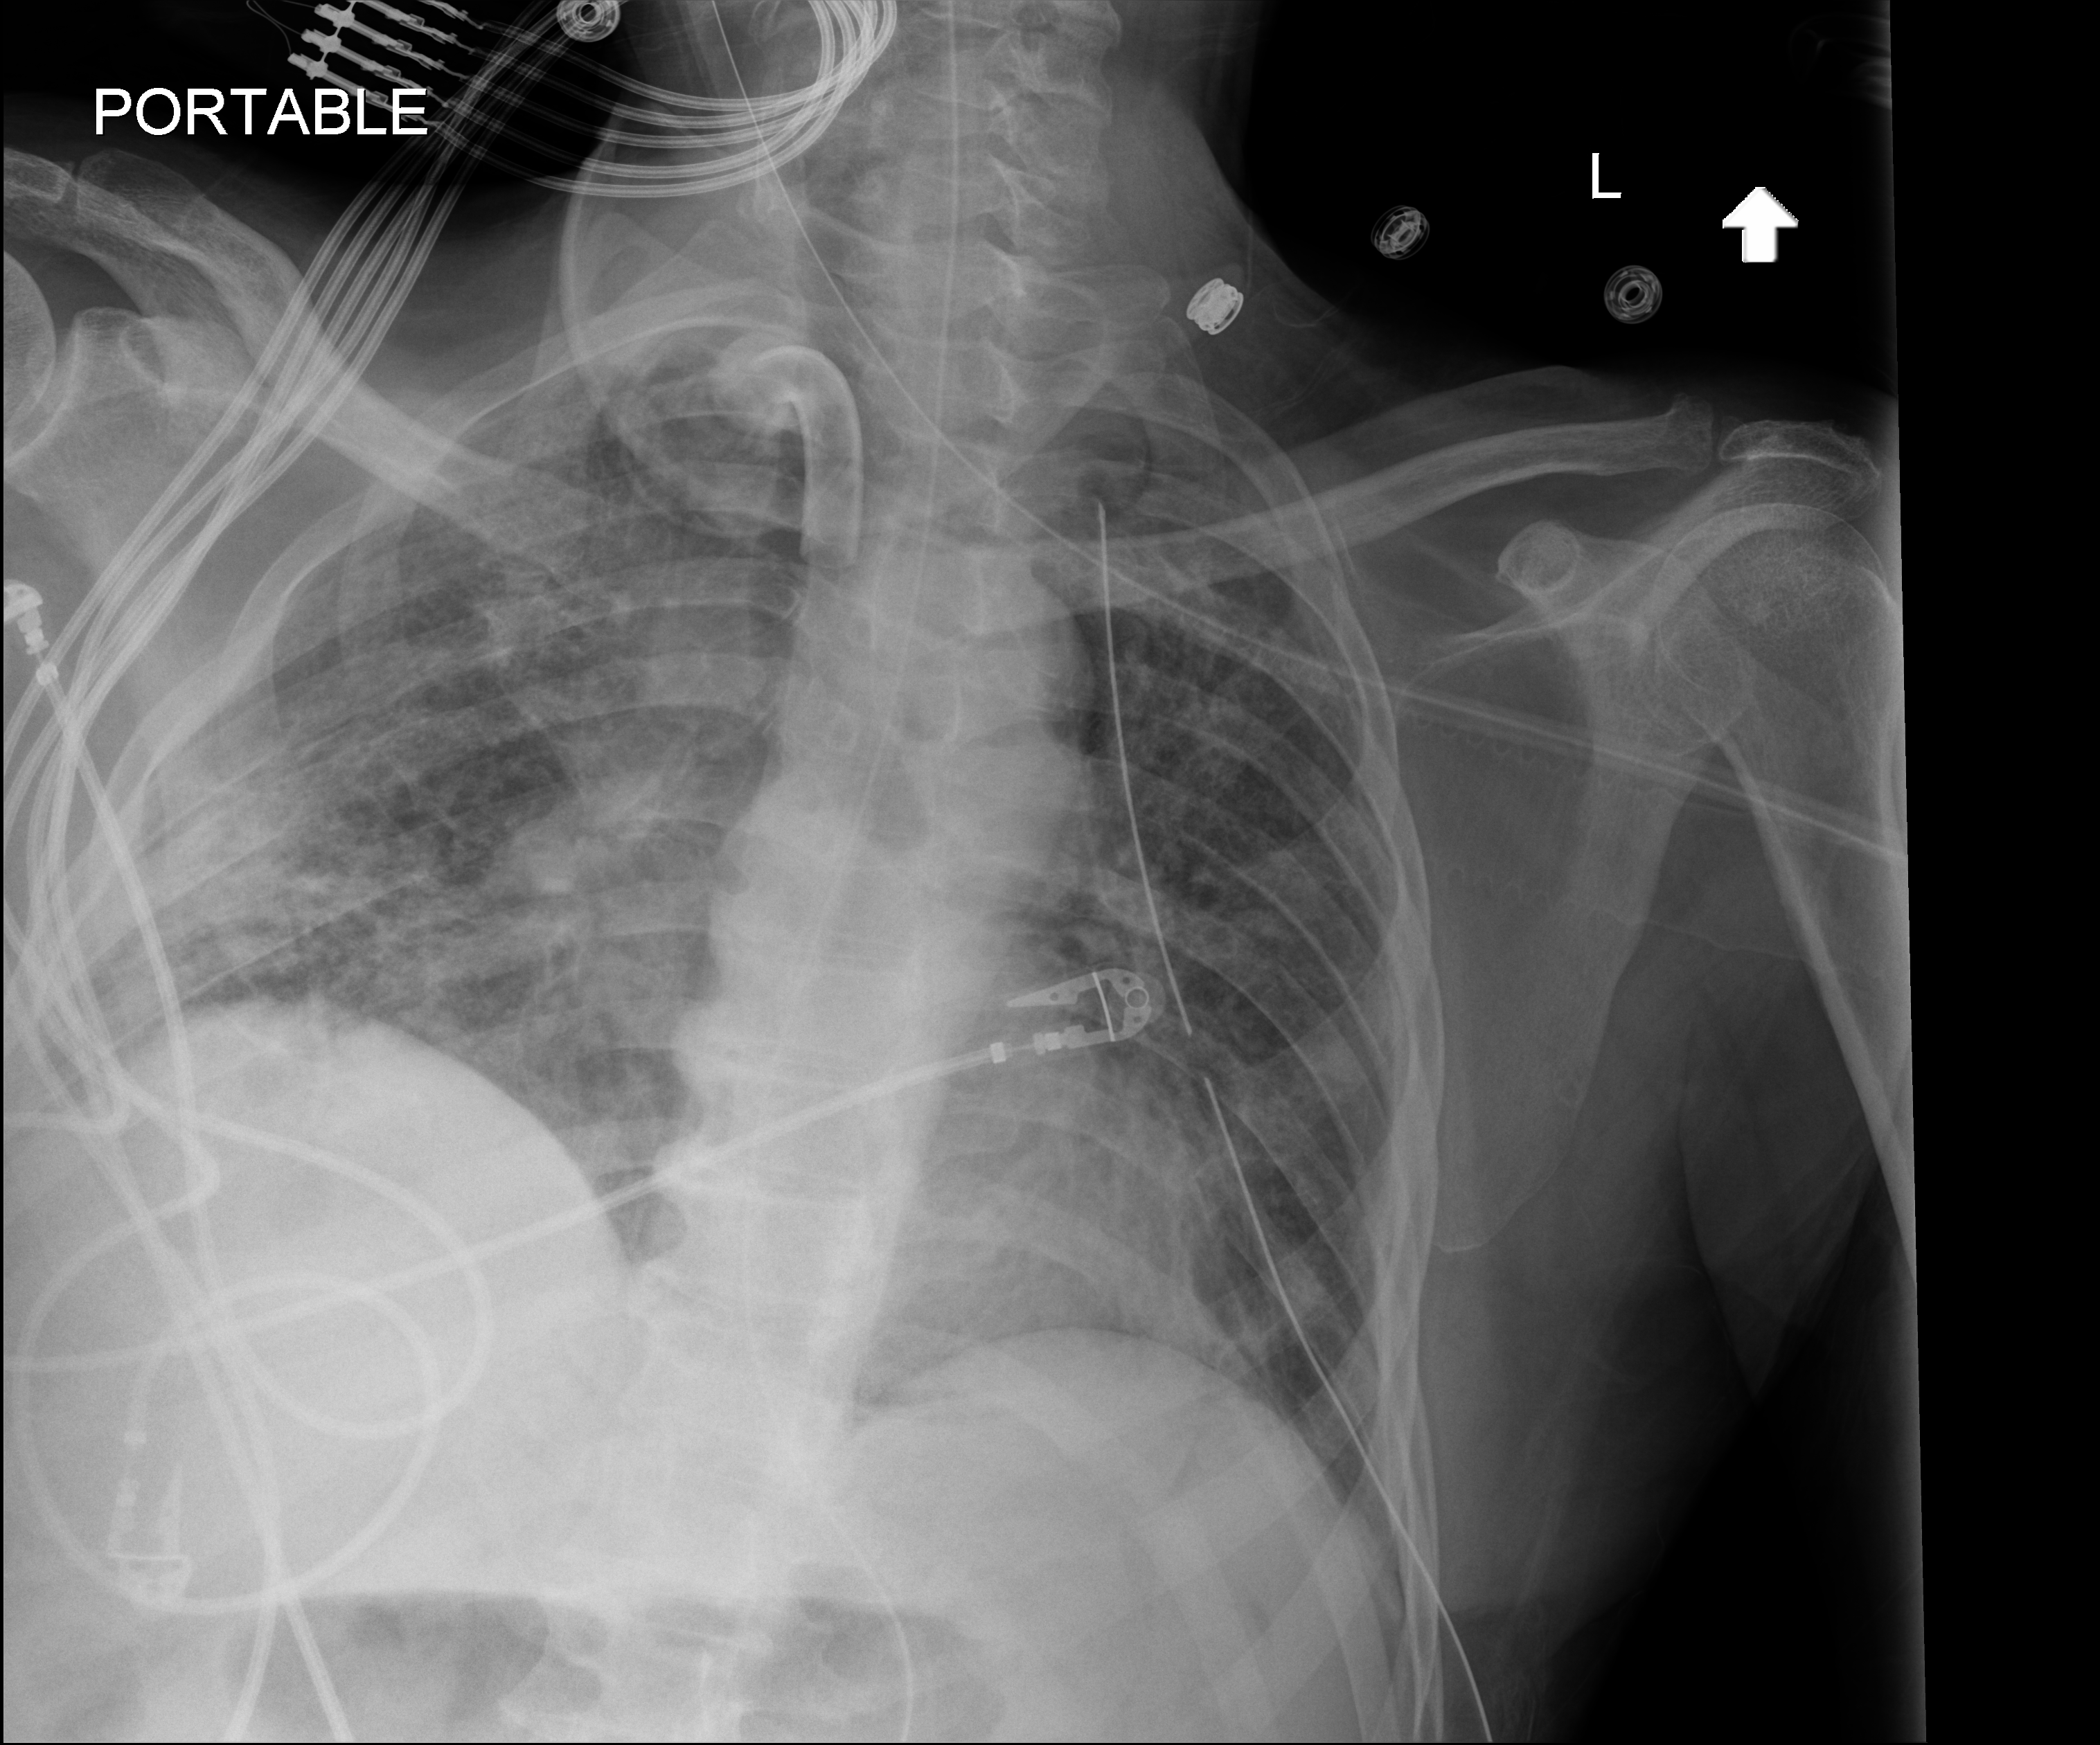
Chest radiograph. Male patient hospitalised with COVID-19, age 18–59 years.
Admission-level facts for this patient (not findings on this image; timing relative to this image not recorded): mechanically ventilated during this hospital stay: yes.